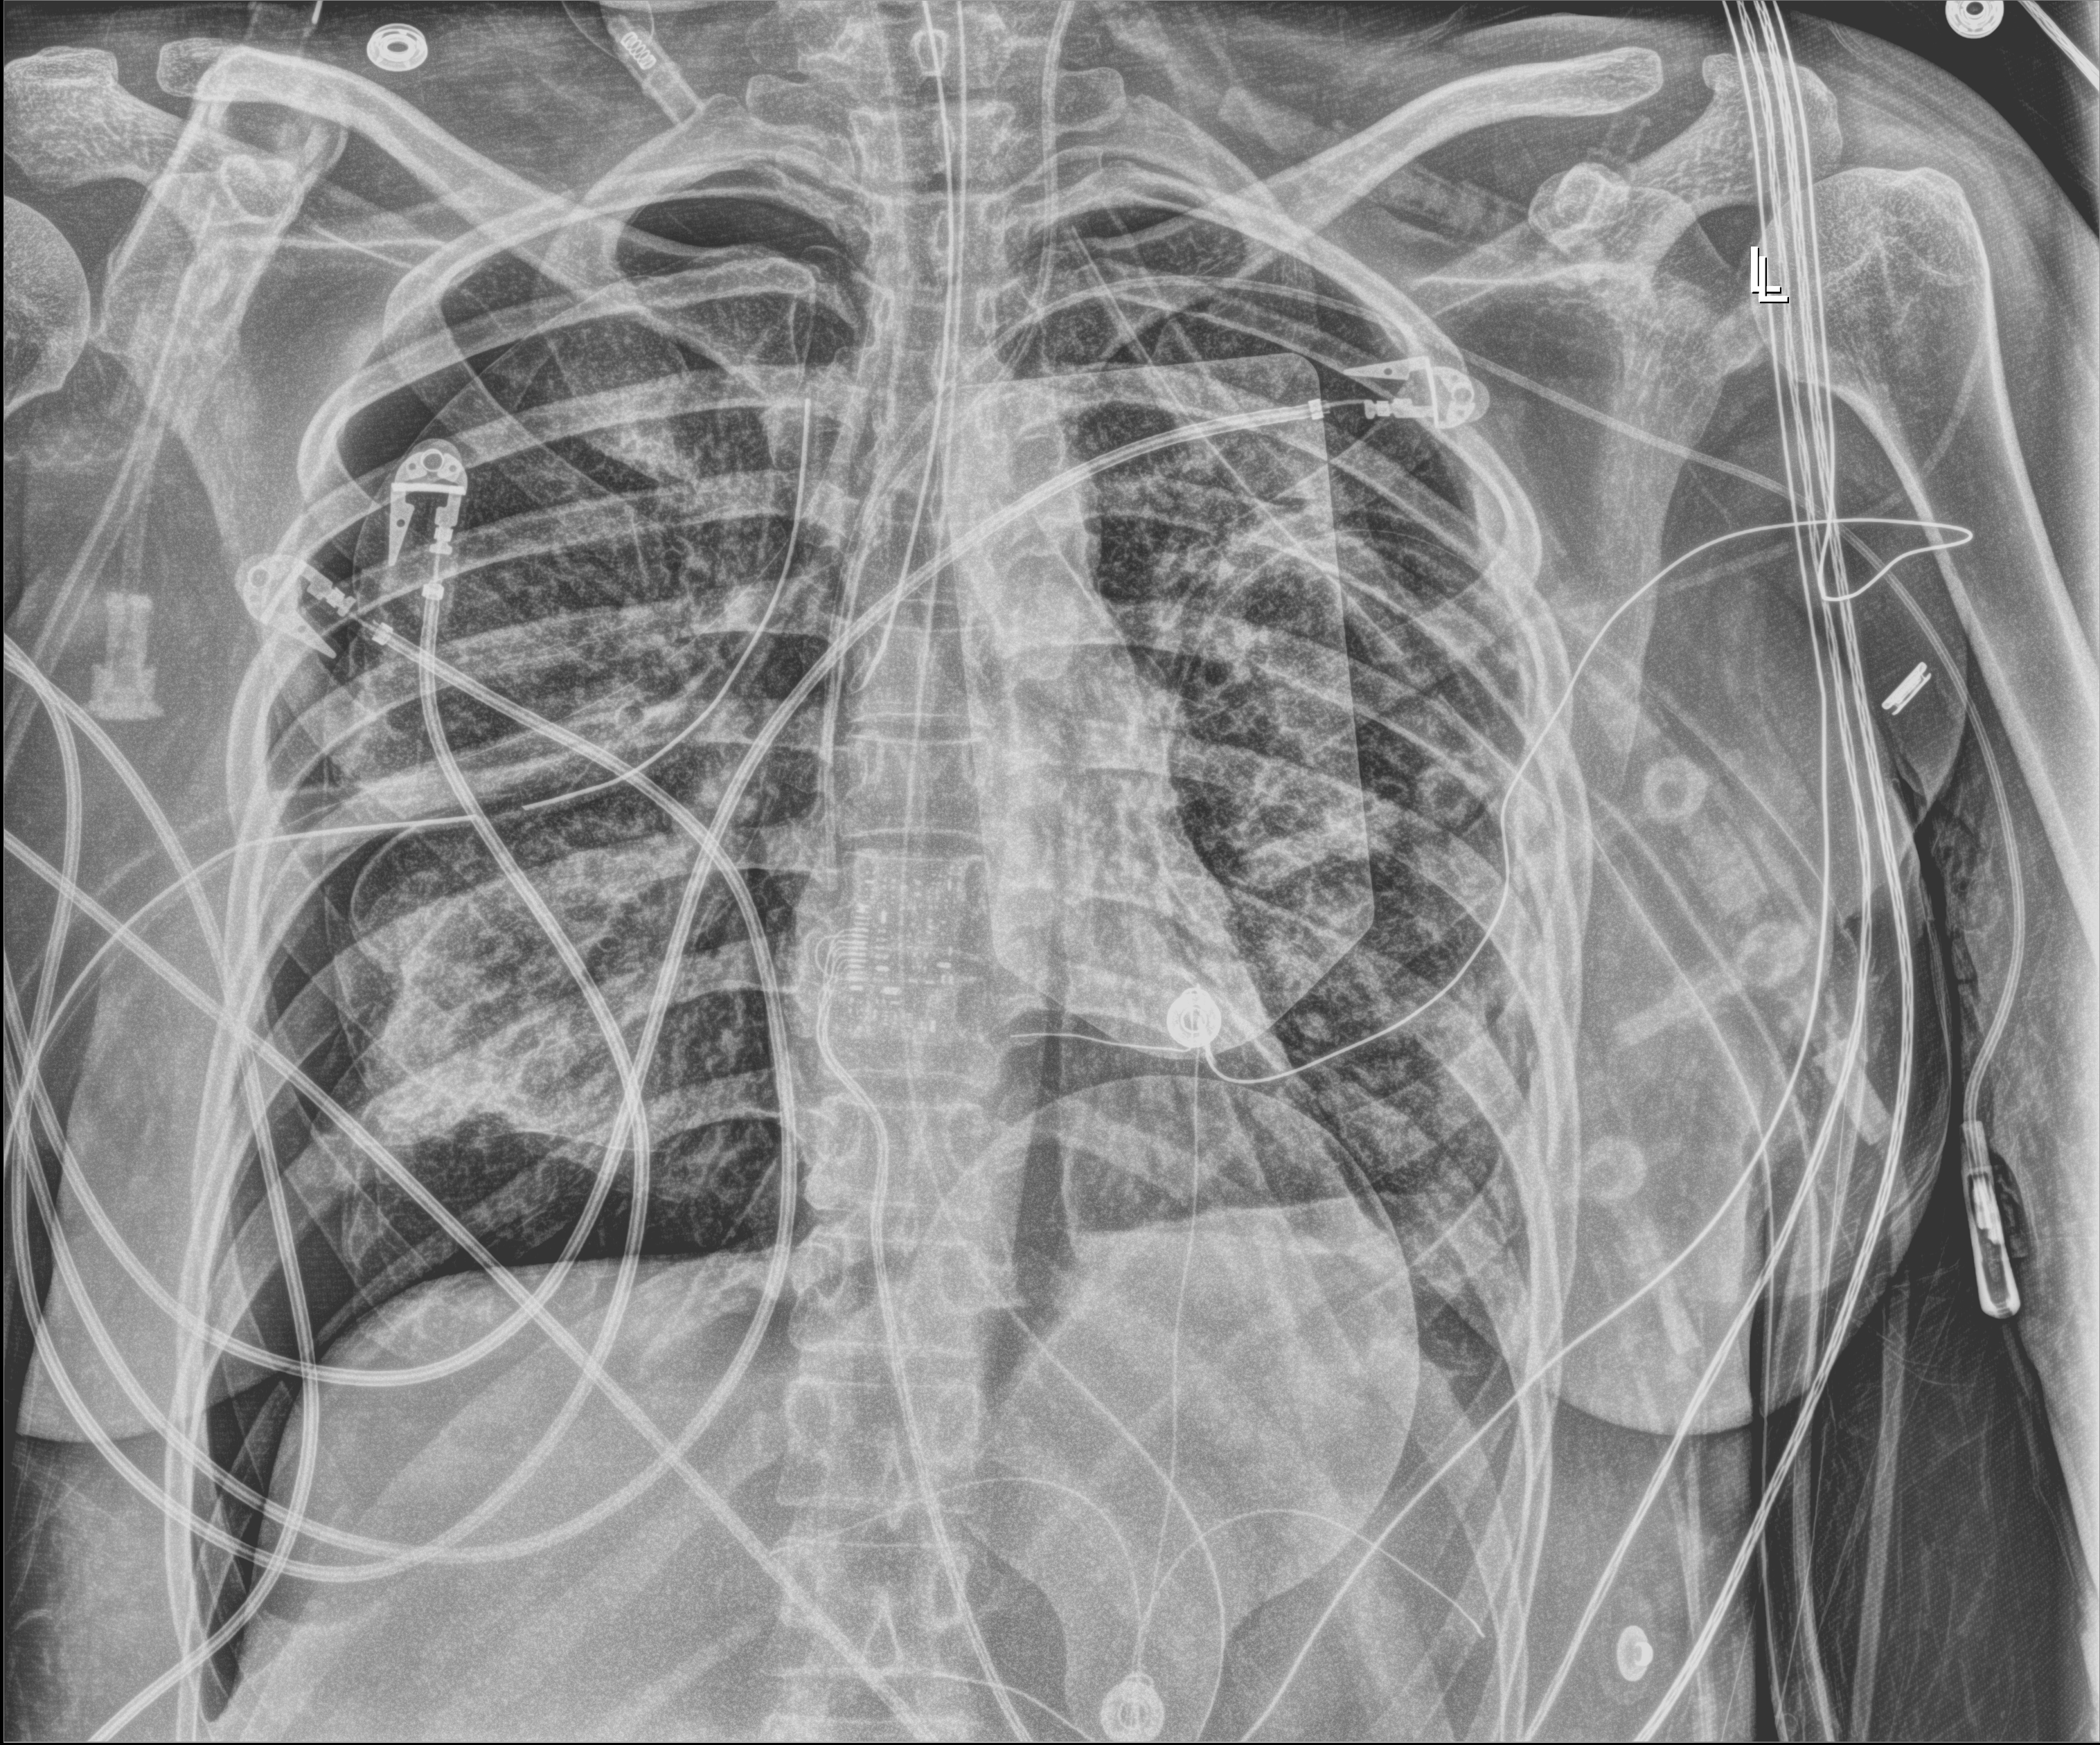
Portable chest radiograph, anteroposterior (AP) projection. Patient hospitalised with COVID-19, aged 18–59 years.
From the hospital-stay record, not from the radiograph (when in the stay this image was taken is not recorded): COPD (admission record): no.